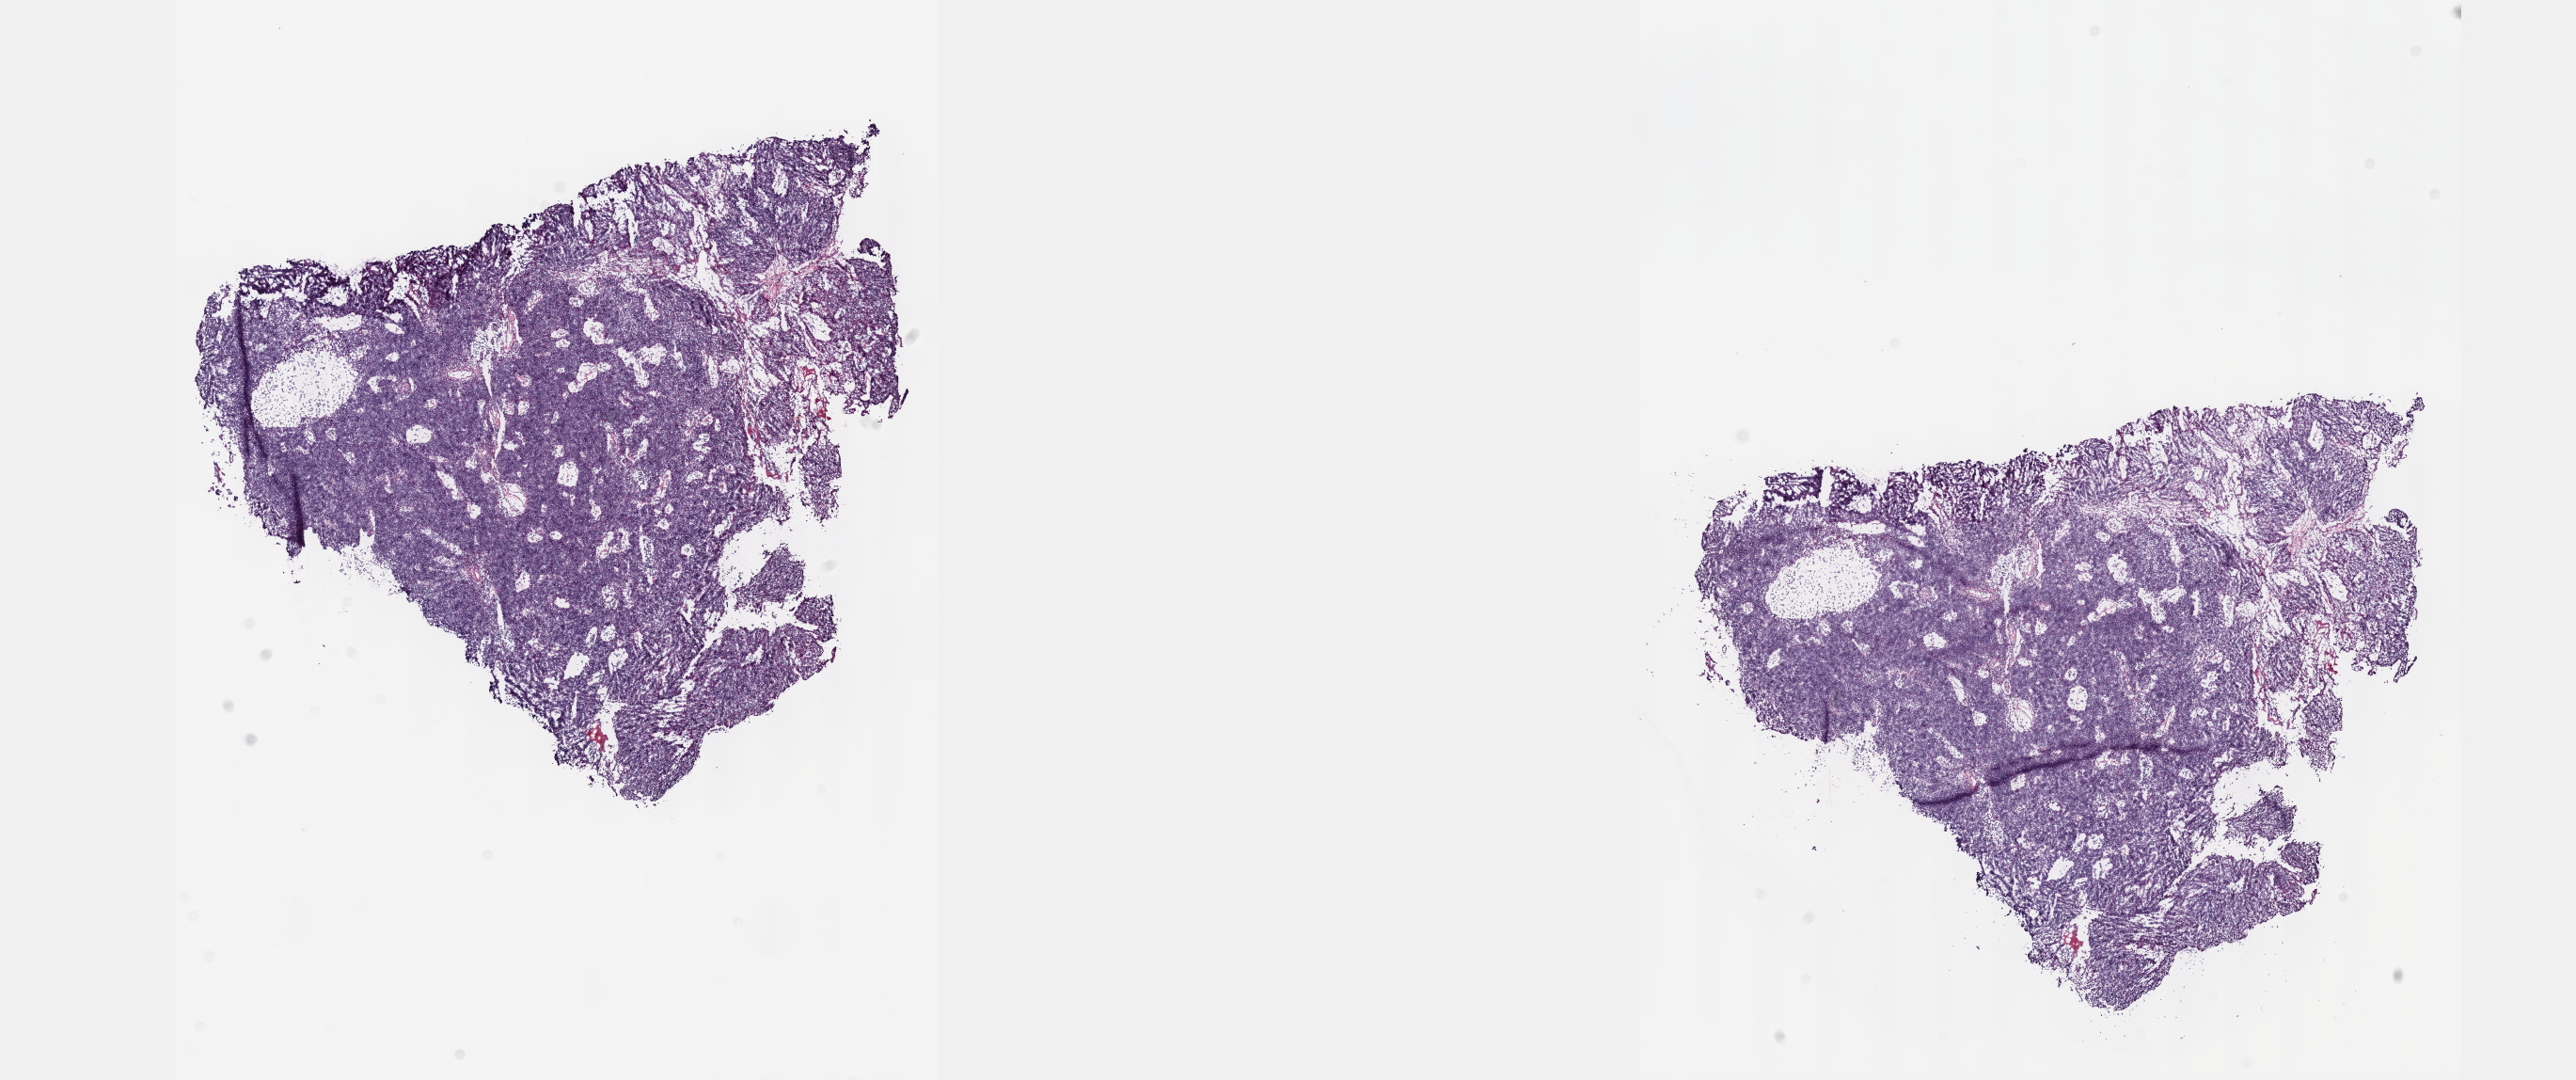
Digitized Hematoxylin and eosin (H&E) stained tissue section (whole slide) — a low-resolution overview of the entire scanned area, about 22.1 x 9.3 mm; frozen section from the top of the tissue portion; sample: primary tumour, thymus. Female, age 69 years at initial diagnosis. Composition of this section per pathologist review: tumour cells 100%, tumour nuclei 80%, normal cells 0%, stromal cells 0%, necrosis 0%. Inflammatory infiltration, as recorded: lymphocyte infiltration 1%, monocyte infiltration 0%, neutrophil infiltration 0%.
Diagnosis: Thymoma, type B2, malignant.